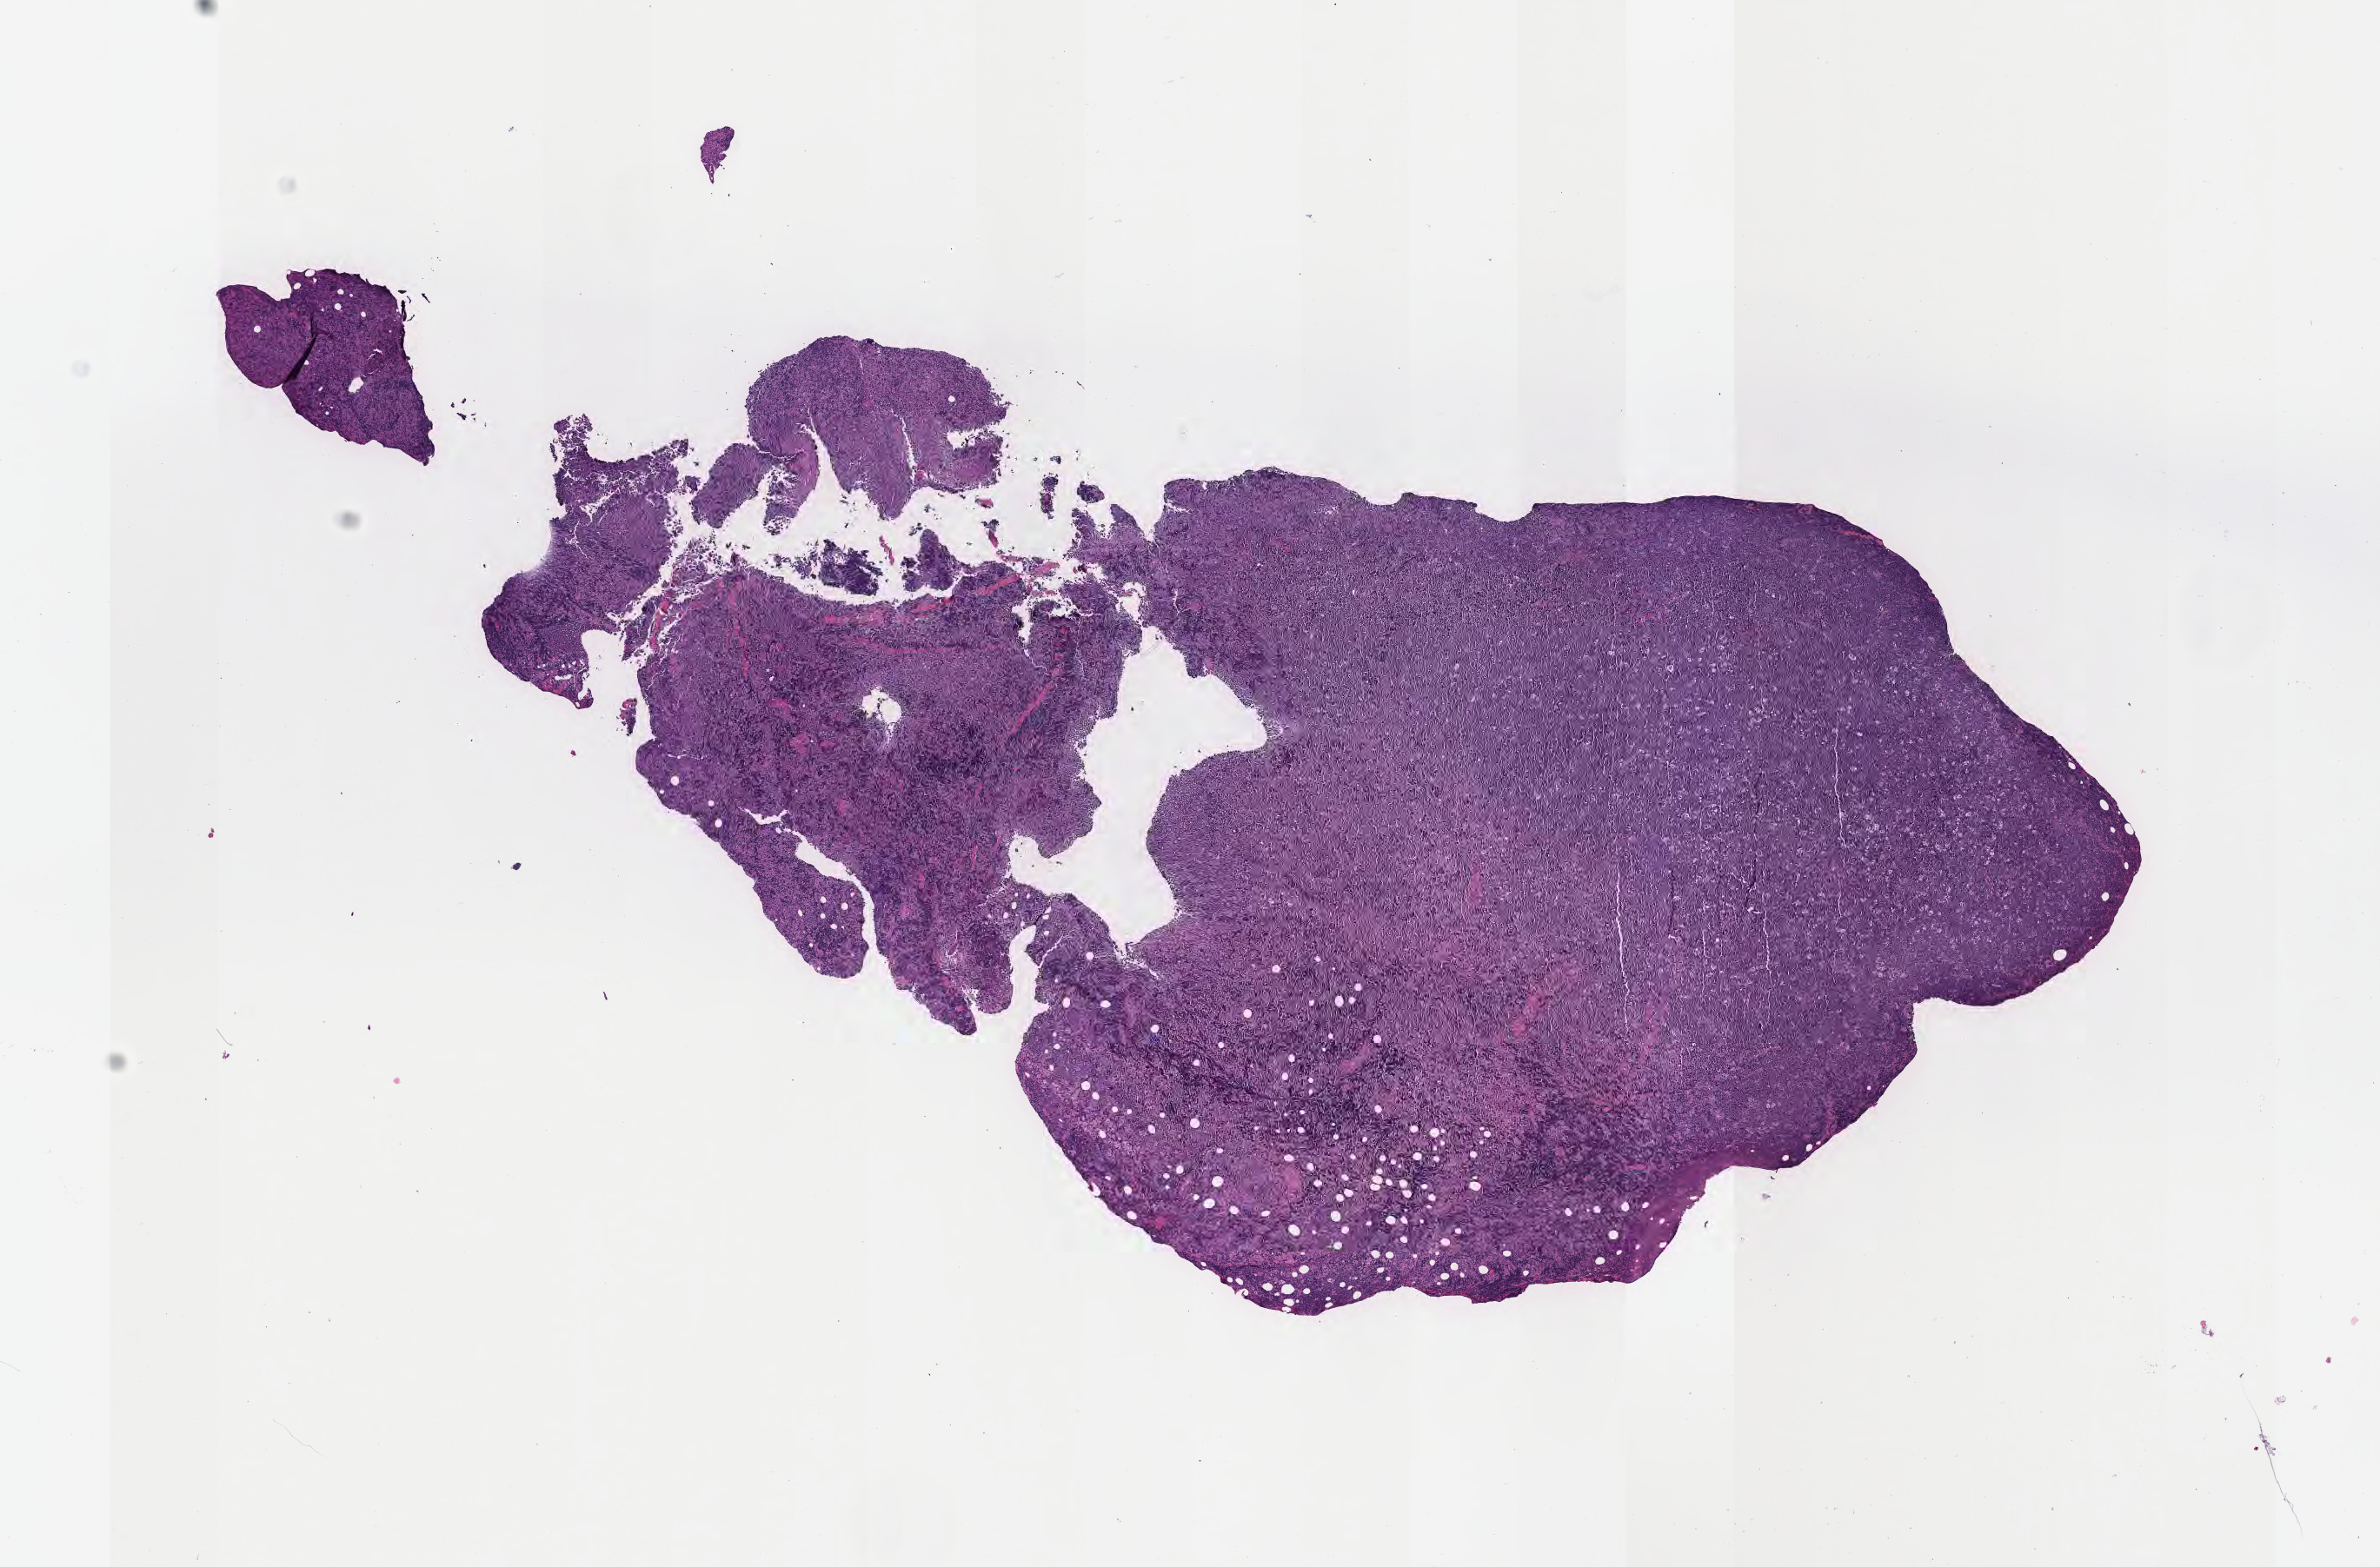
Whole-slide image, H&E stain, low-resolution overview of the scanned area, about 11.1 x 7.3 mm. Formalin-fixed, paraffin-embedded (FFPE) tissue. Specimen: primary tumor. Patient female; 40 years old. Pathologist review of this section (percent, as recorded): tumor cells 90%, tumor nuclei 90%, stromal cells 5%, necrosis 5%, normal cells 0%. Infiltration values recorded for this section: lymphocyte infiltration 10%, monocyte infiltration 40%, neutrophil infiltration 5%.
- section: top of the tissue portion
- Ann Arbor stage (patient): Stage III
- histologic diagnosis: Burkitt lymphoma, NOS